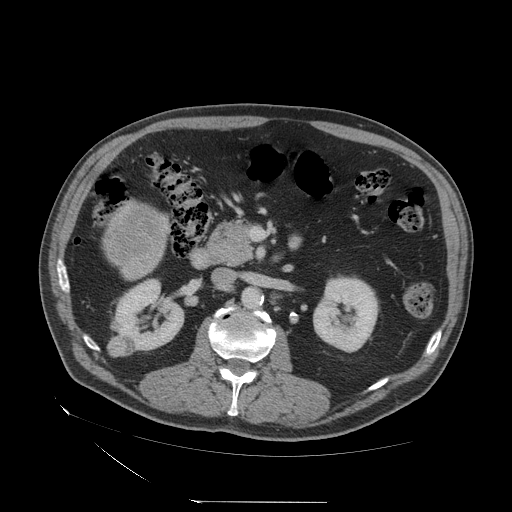
Contrast-enhanced abdominal CT (liver protocol), one axial slice. Slice 7 of 83 in the series (ordered by position). Reconstruction kernel STANDARD. 140 kVp. Soft-tissue window (W 400 / L 40 HU). 2.5 mm slice thickness. 512 × 512 image matrix, field of view 460 × 460 mm. Case-level facts recorded for this patient, not image findings: diagnosis: hepatocellular carcinoma (patient treated with transarterial chemoembolisation; whether this scan precedes or follows treatment is not stated here); TNM stage (as recorded): Stage-I; Child-Pugh class: A.
Annotated regions visible in this slice (semi-automatically segmented with operator editing):
- mass: bounding box <103,205,171,265> (left, top, right, bottom; pixels)